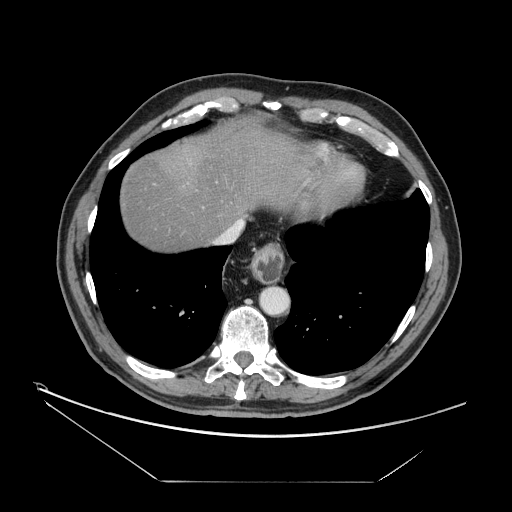
Contrast-enhanced abdominal CT, one axial slice. Position 142 of 161 along the scan axis. Reconstruction kernel STANDARD. 120 kVp. Intravenous contrast given. Soft-tissue window (W 400 / L 40 HU). 2.5 mm slice thickness. 512 × 512 image matrix. Male patient, age 65 years. From the clinical record (not read from this slice): diagnosis: colorectal cancer liver metastases, imaged before liver resection; multiple liver metastases: yes; largest metastasis: 4.2 cm; disease in both lobes: yes.
Outlined on this slice (manually delineated by an expert):
- hepatic veins: box from (x=220, y=219) to (x=244, y=243) px
- liver: (x=119, y=122)–(x=304, y=251)
- planned liver remnant (the part of the liver to remain after resection): (x=119, y=122)–(x=304, y=251)